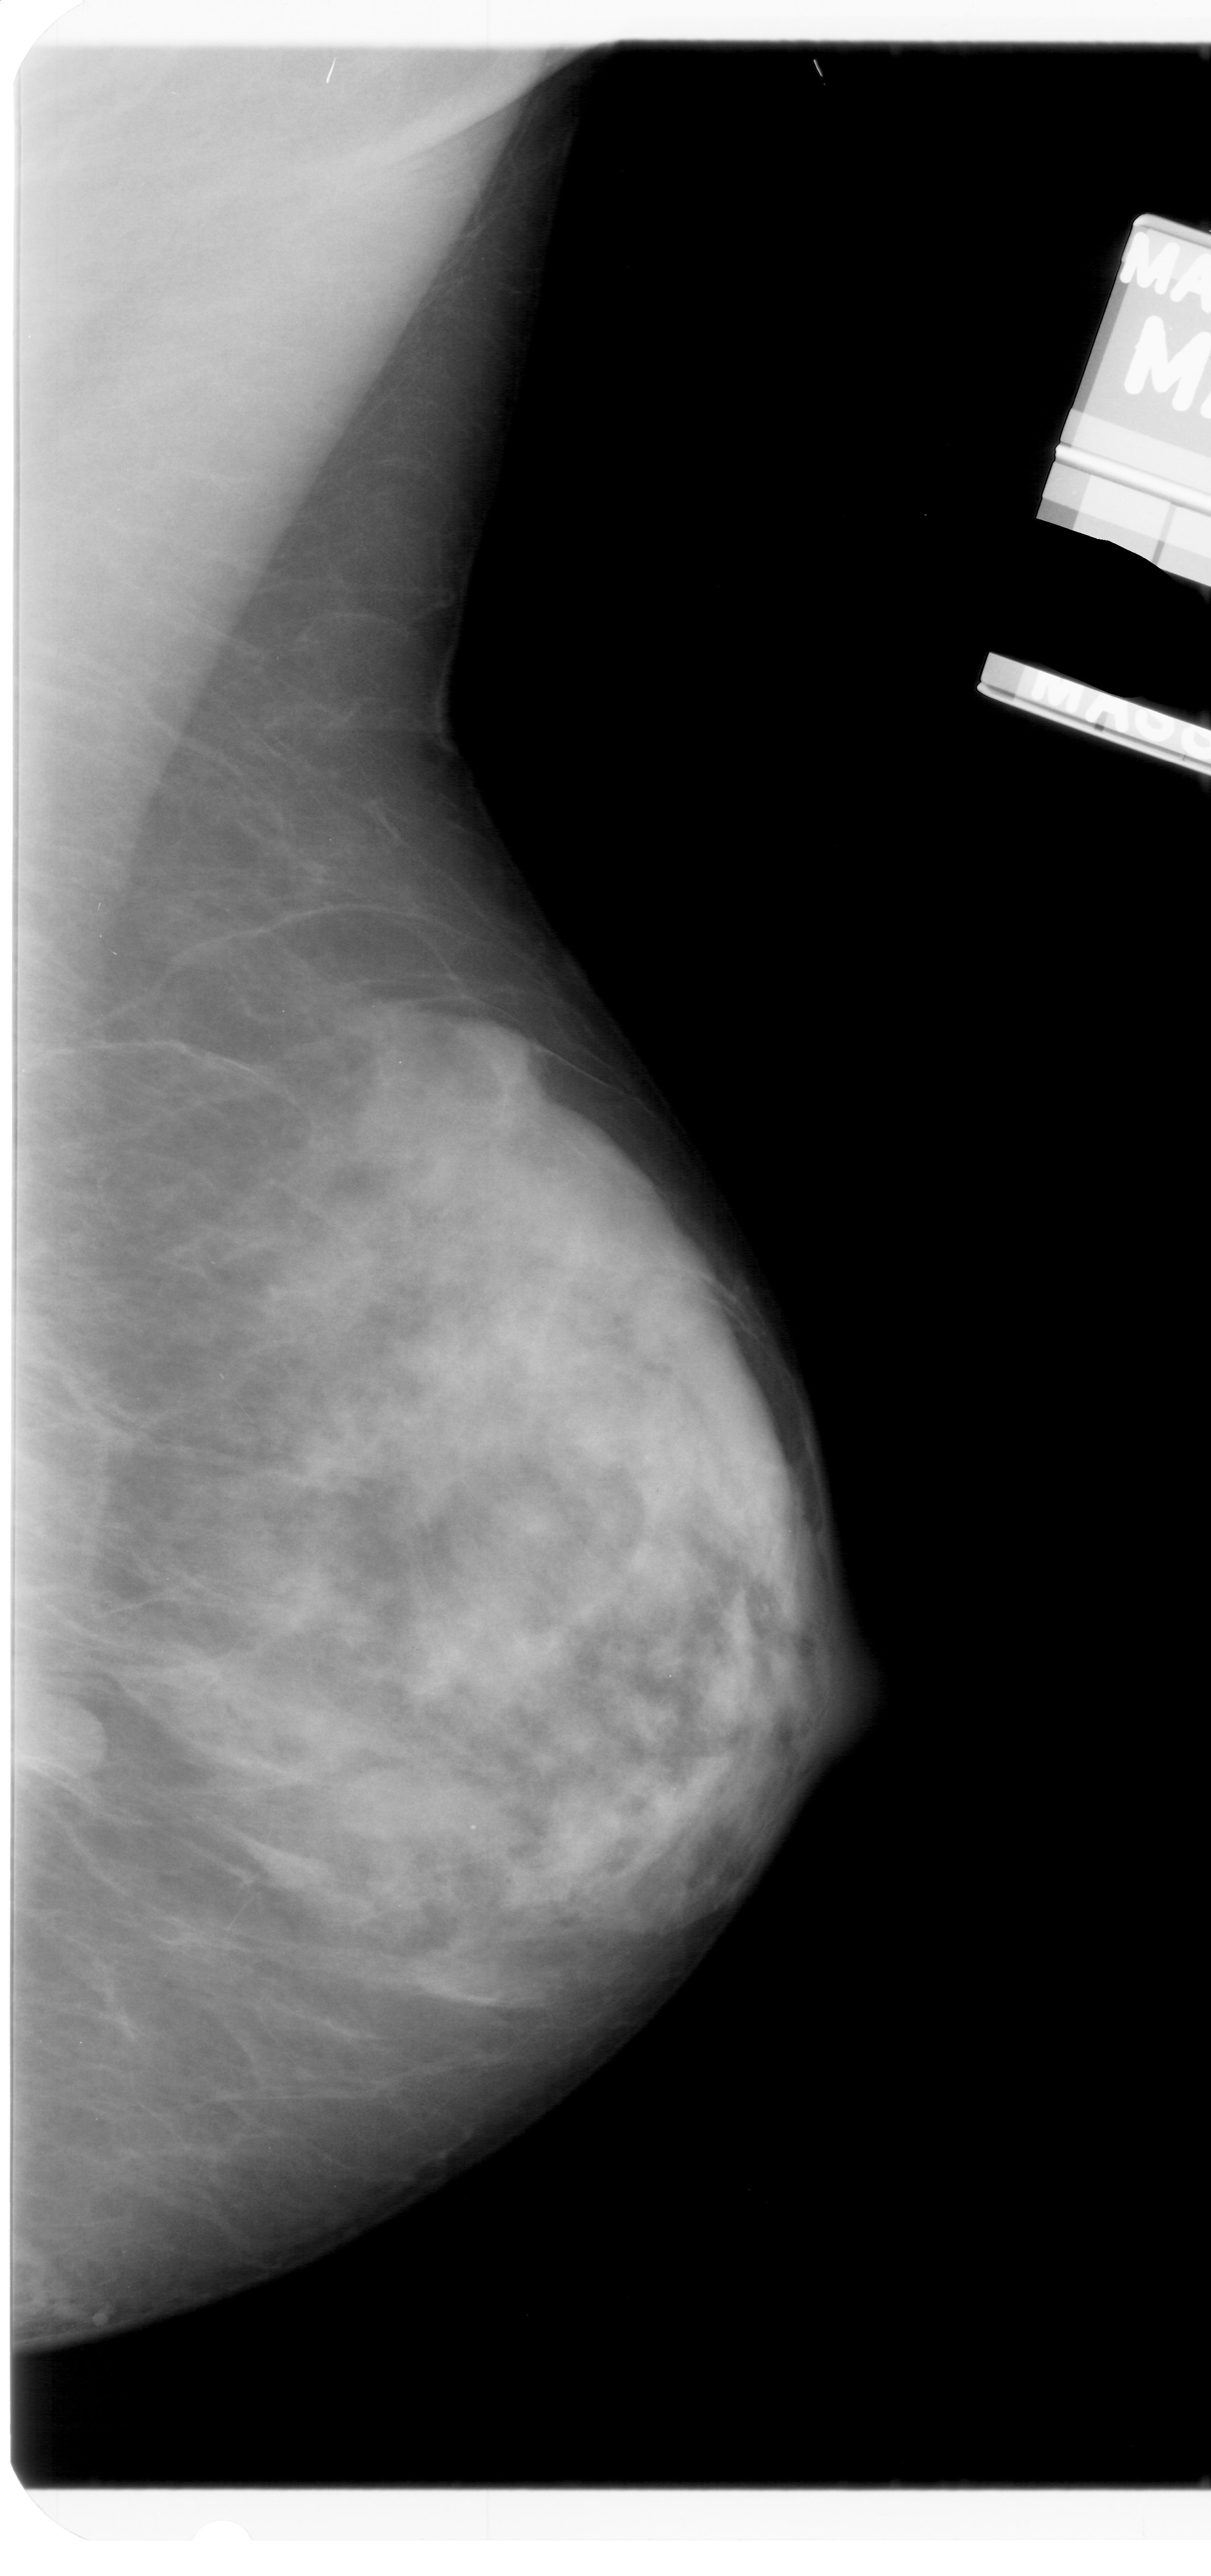
Digitized screen-film mammogram, right breast, mediolateral oblique (MLO) view, BI-RADS breast density category 4 (scale 1–4).
Mass, shape oval, margins obscured; BI-RADS assessment category 3; pathology (as recorded): benign.